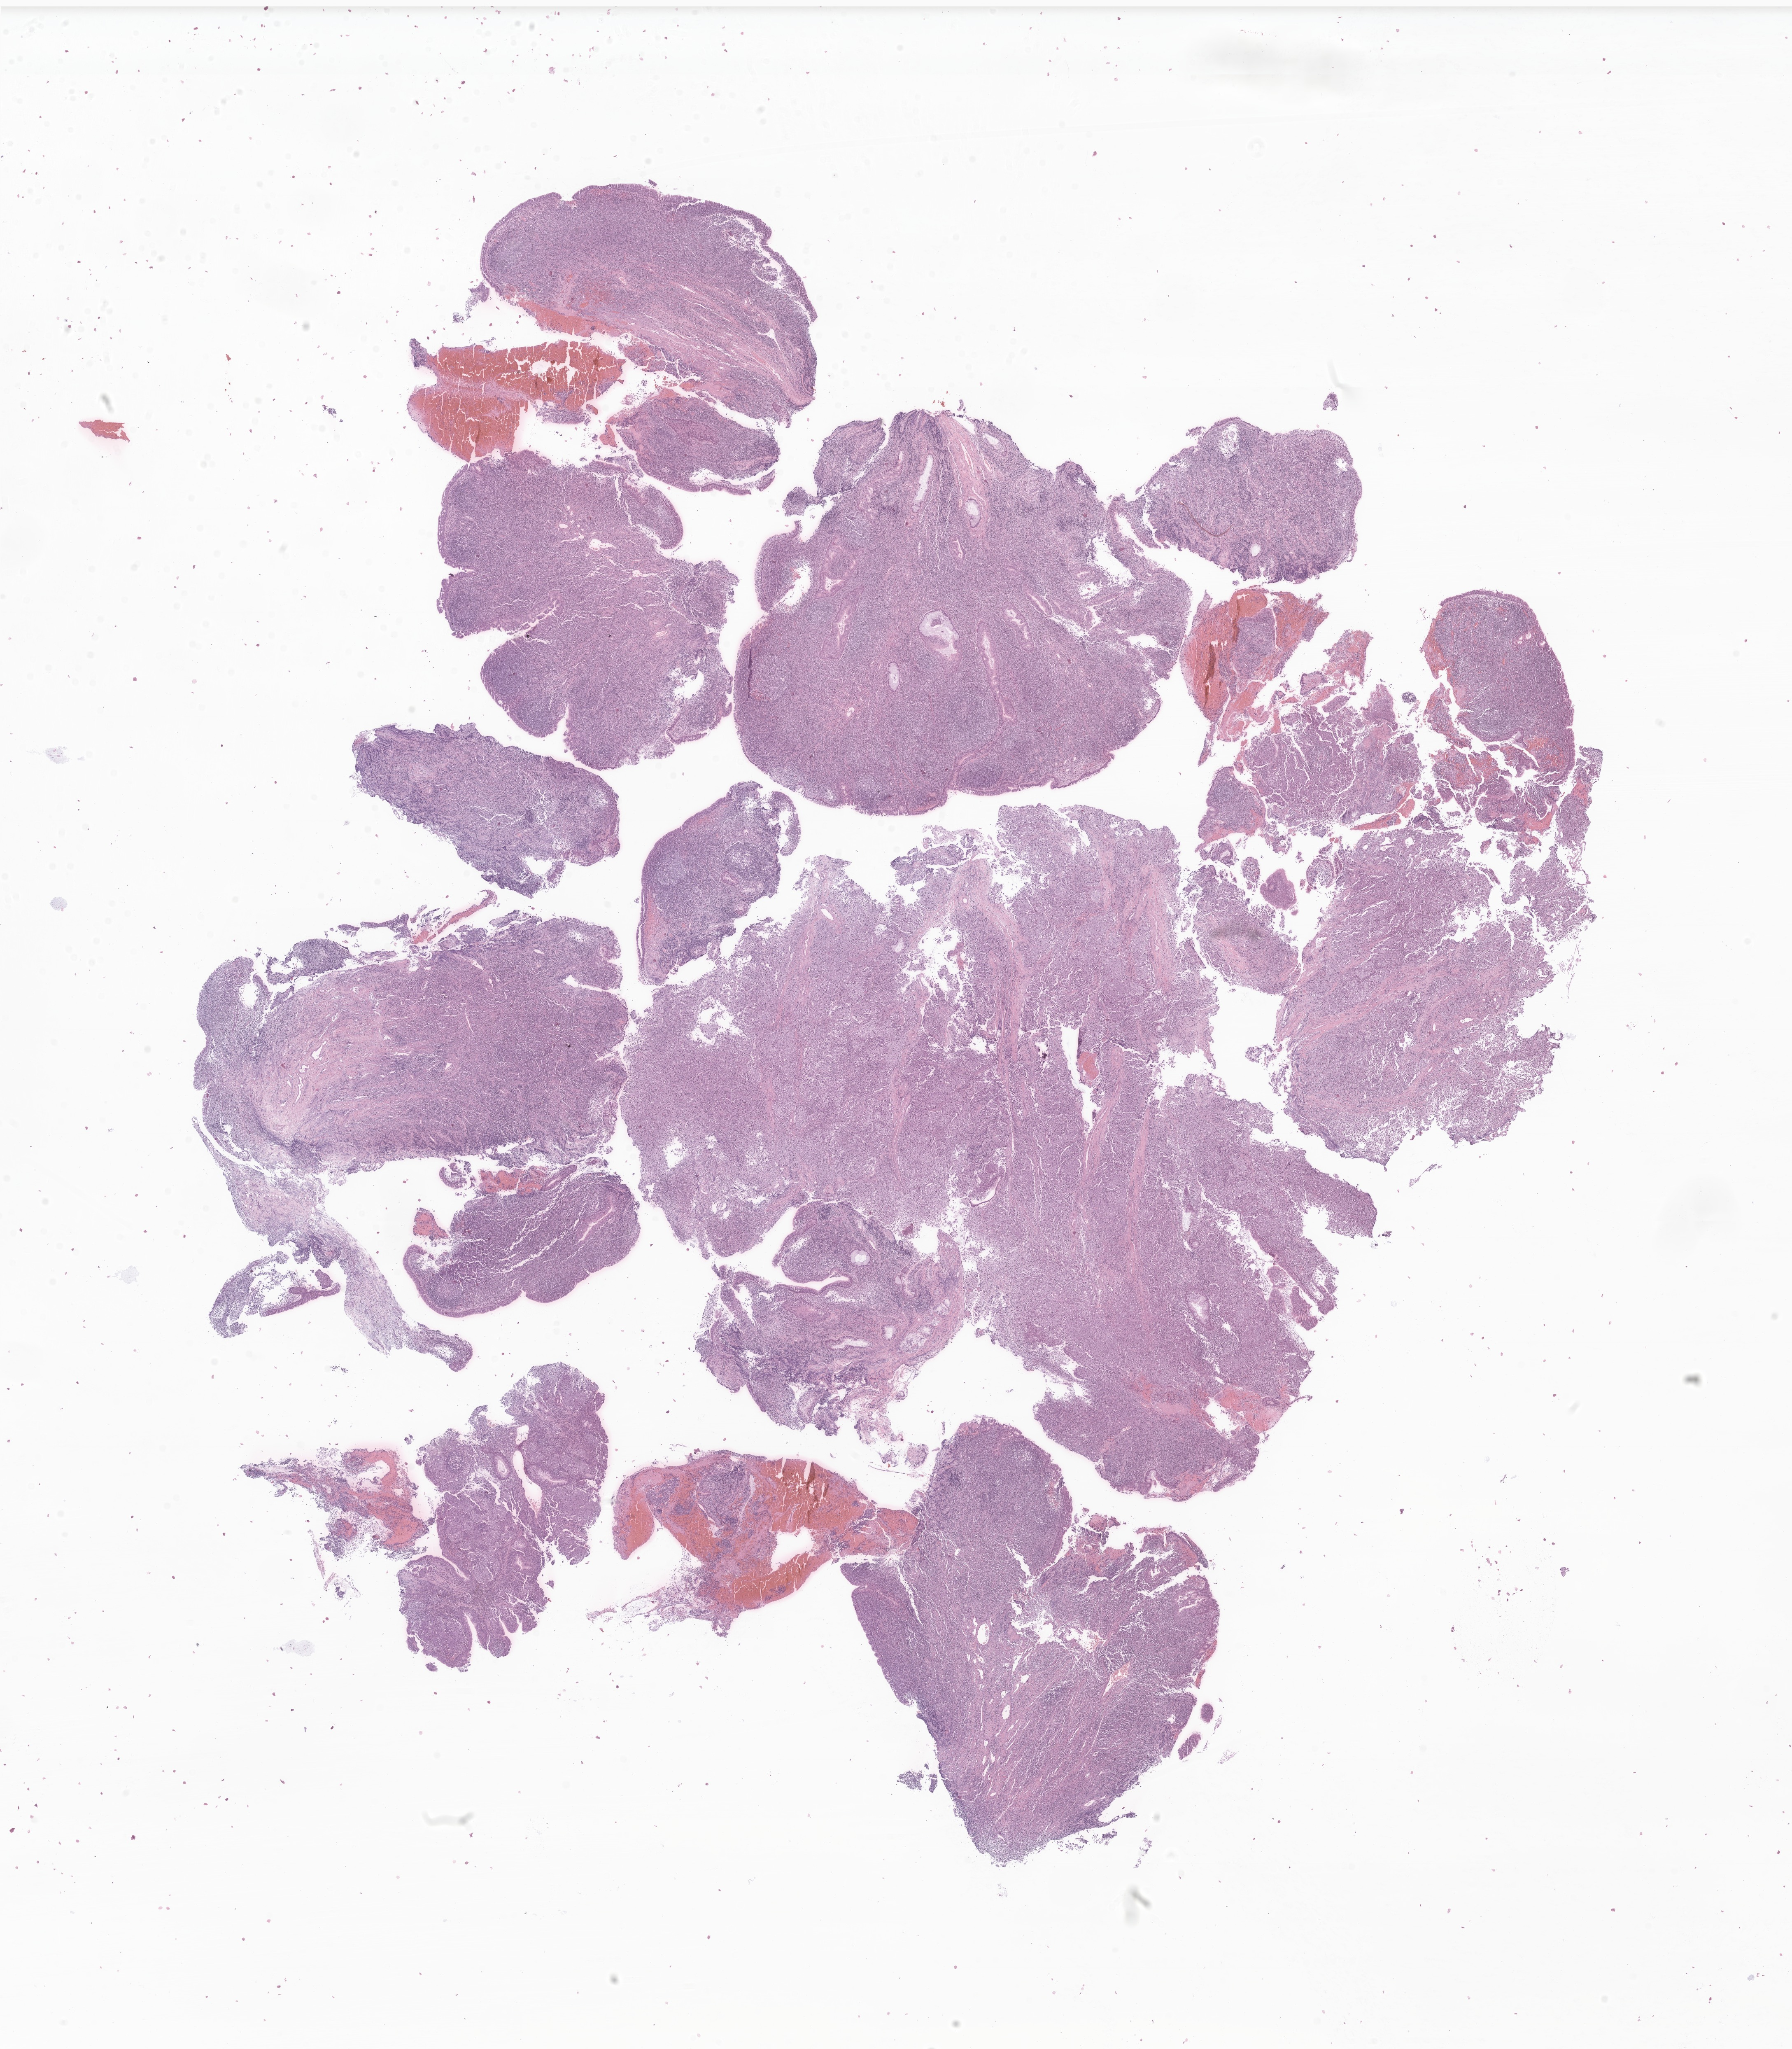
Hematoxylin and eosin (H&E) whole-slide image of tumor tissue from the nasopharynx — a low-resolution overview of the entire scanned area, about 18.4 x 21.0 mm, formalin-fixed paraffin-embedded section. Patient: male, age 105 months (8 years 9 months).
• diagnosis: Squamous cell carcinoma, NOS